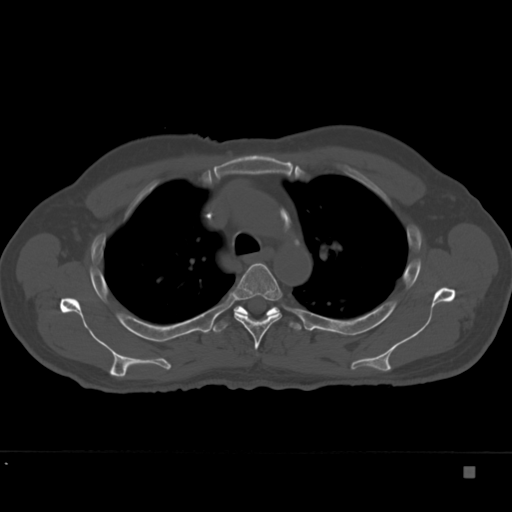
CT including the spine, one axial slice; slice 267 of 332 in the series (ordered by position); reconstruction kernel Br40s; bone window (W 1800 / L 400 HU); 1.5 mm slice thickness; 512 × 512 image matrix, field of view 389 × 389 mm. Patient: male, 72 years. Case-level facts recorded for this patient, not image findings: primary cancer: skeletal.
Outlined on this slice (semi-automatic segmentation, software-assisted and operator-edited):
- T4 vertebra: box from (x=231, y=263) to (x=283, y=350) px
- T5 vertebra: (x=213, y=306)–(x=302, y=333)